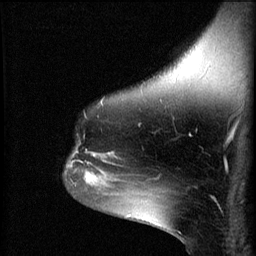
Breast MRI (dynamic contrast-enhanced), one sagittal slice. Position 45 of 60 along the scan axis. 3 images stored at this slice position (order not interpretable as contrast timing). 1.5 T. TE 4.2 ms, TR 8.2 ms. 2 mm slice thickness. 256 × 256 image matrix, field of view 180 × 180 mm. Female patient, age 49 years.
Structures marked on this image (semi-automatic segmentation, software-assisted and operator-edited):
- analysis volume of interest (the breast-tissue region the enhancement analysis was run in; not a lesion): bounding box [x1, y1, x2, y2] px = [65, 140, 109, 187]
- tumour enhancement mask (voxels above the 70 % enhancement threshold inside the analysis volume of interest): [68, 152, 109, 187]